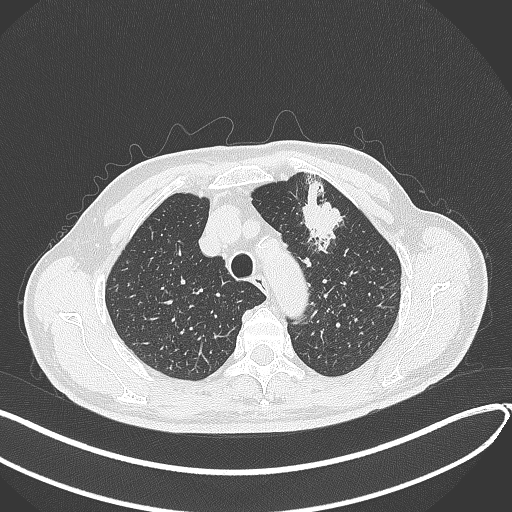
Chest CT, one axial slice. Position 334 of 459 along the scan axis. Lung window (W 1500 / L -600 HU). 512 × 512 image matrix, field of view 400 × 400 mm. Patient: male, 74 years. From the clinical record (not read from this slice): clinical TNM (as recorded): T2b N0 M1c.
Structures marked on this image (rectangle marked by the reading radiologist):
- lung tumour (recorded histology: adenocarcinoma): box from (x=292, y=175) to (x=348, y=253) px